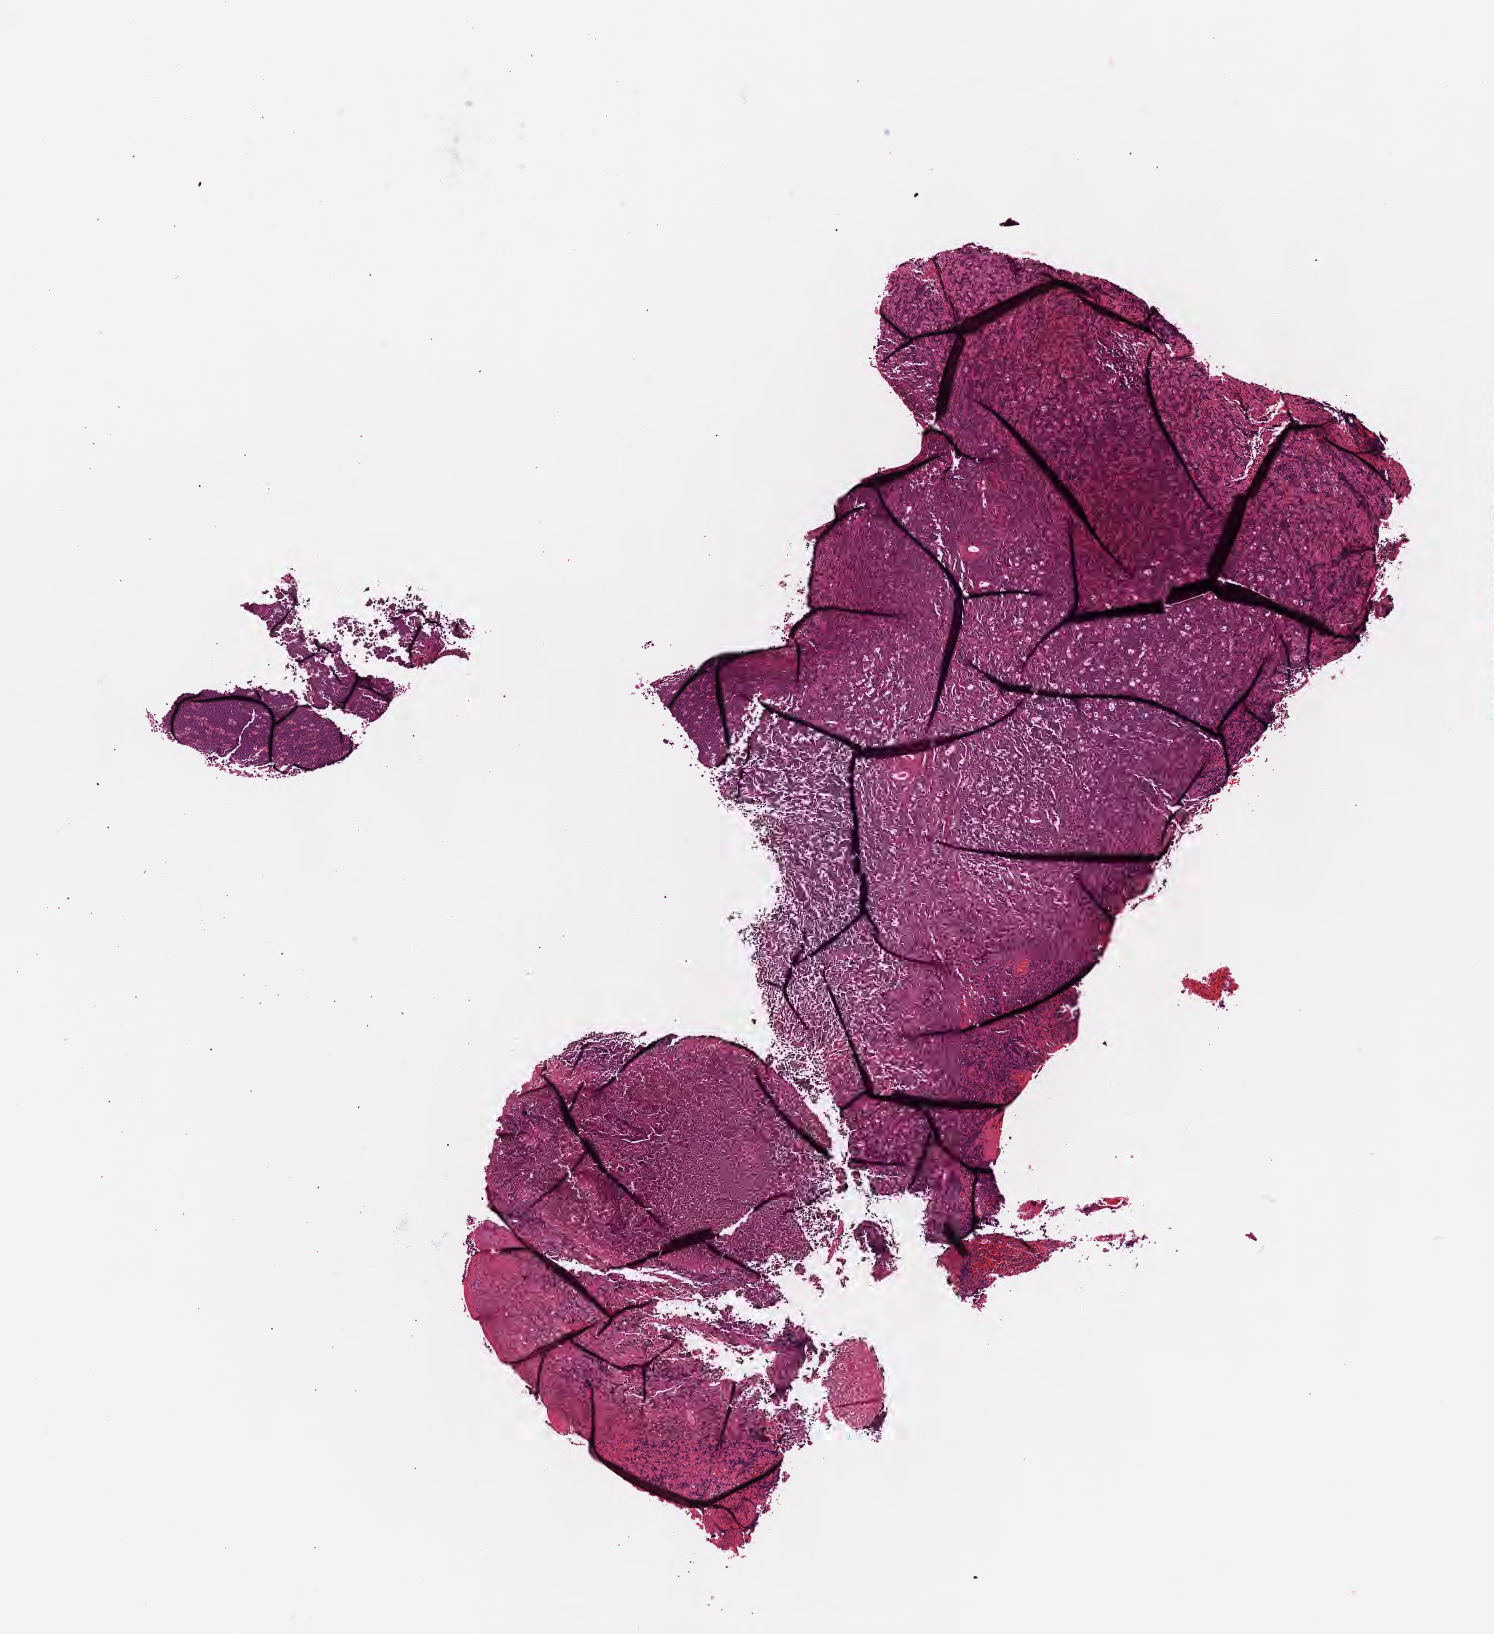
Digitized hematoxylin and eosin (H&E)-stained section, a low-resolution overview of the entire scanned area, about 6.0 x 6.6 mm; FFPE section; primary tumor. Male patient; age at initial diagnosis 3 years. Pathologist review of this section (percent, as recorded): tumor cells 85%, tumor nuclei 90%, stromal cells 10%, necrosis 5%, normal cells 0%. Inflammatory infiltration, as recorded: lymphocyte infiltration 75%, monocyte infiltration 20%, neutrophil infiltration 0%.
* diagnosis: Burkitt lymphoma, NOS
* section: bottom of the tissue portion
* Ann Arbor stage (patient): Stage II